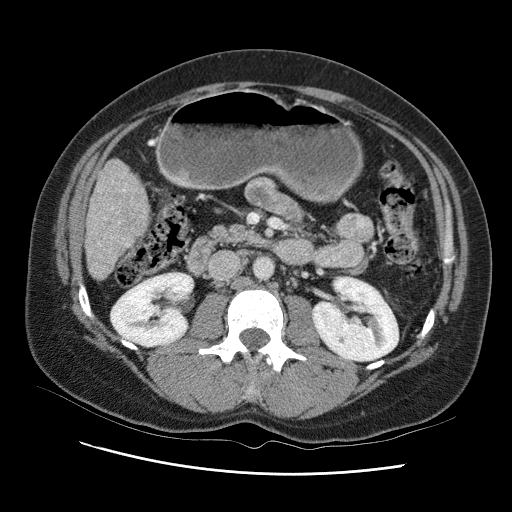
Contrast-enhanced abdominal CT (liver protocol), one axial slice. Position 29 of 95 along the scan axis. Reconstruction kernel STANDARD. 120 kVp. One of 2 acquisitions stored at this slice position. Soft-tissue window (W 400 / L 40 HU). 2.5 mm slice thickness. 512 × 512 image matrix, field of view 360 × 360 mm. From the clinical record (not read from this slice): diagnosis: hepatocellular carcinoma (patient treated with transarterial chemoembolisation; whether this scan precedes or follows treatment is not stated here); TNM stage (as recorded): Stage-I; Child-Pugh class: B; tumour differentiation: moderately differentiated; tumour nodularity: uninodular.
Annotated regions visible in this slice (semi-automatic segmentation, software-assisted and operator-edited):
- liver parenchyma outside the tumour (the mass and vessels are separate outlines, so this box may not span the whole liver): box from (x=86, y=148) to (x=161, y=280) px
- liver vessels: (x=101, y=189)–(x=133, y=251)